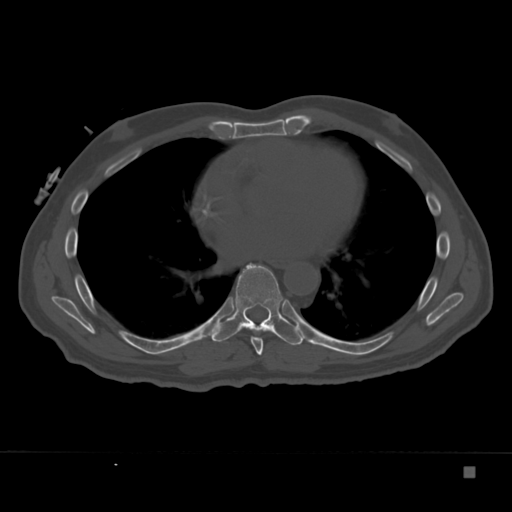
CT including the spine, one axial slice. Slice 212 of 332 in the series (ordered by position). 120 kVp. Bone window (W 1800 / L 400 HU). 1.5 mm slice thickness. 512 × 512 image matrix, field of view 389 × 389 mm. Patient: male, 72 years. From the clinical record (not read from this slice): primary cancer: skeletal.
Outlined on this slice (semi-automatic segmentation, software-assisted and operator-edited):
- T7 vertebra: box from (x=251, y=337) to (x=263, y=355) px
- T8 vertebra: (x=211, y=264)–(x=308, y=346)